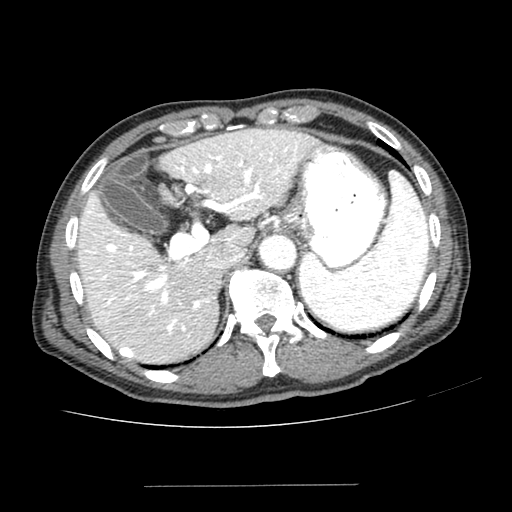
Contrast-enhanced abdominal CT (liver protocol), one axial slice; 100 kVp; one of 2 acquisitions stored at this slice position; soft-tissue window (W 400 / L 40 HU); 512 × 512 image matrix, field of view 360 × 360 mm. Case-level facts recorded for this patient, not image findings: diagnosis: hepatocellular carcinoma (patient treated with transarterial chemoembolisation; whether this scan precedes or follows treatment is not stated here); TNM stage (as recorded): Stage-I; Child-Pugh class: A; tumour differentiation: poorly differentiated.
Structures marked on this image (semi-automatically segmented with operator editing):
- liver parenchyma outside the tumour (the mass and vessels are separate outlines, so this box may not span the whole liver): box from (x=78, y=130) to (x=312, y=362) px
- liver vessels: (x=83, y=135)–(x=298, y=355)